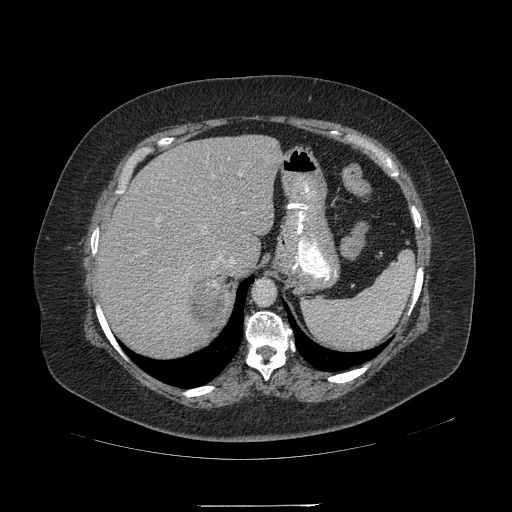
Contrast-enhanced abdominal CT, one axial slice; slice 164 of 217 in the series (ordered by position); reconstruction kernel STANDARD; 120 kVp; intravenous contrast given; soft-tissue window (W 400 / L 40 HU); 512 × 512 image matrix. Patient: female, 55 years. Case-level facts recorded for this patient, not image findings: diagnosis: adrenocortical carcinoma; tumour side: right adrenal; tumour size at pathology: 11 cm; Ki-67 index: 20 %; stage (as recorded): 2.
Outlined on this slice (semi-automatic segmentation, software-assisted and operator-edited):
- mass: box from (x=192, y=279) to (x=225, y=326) px